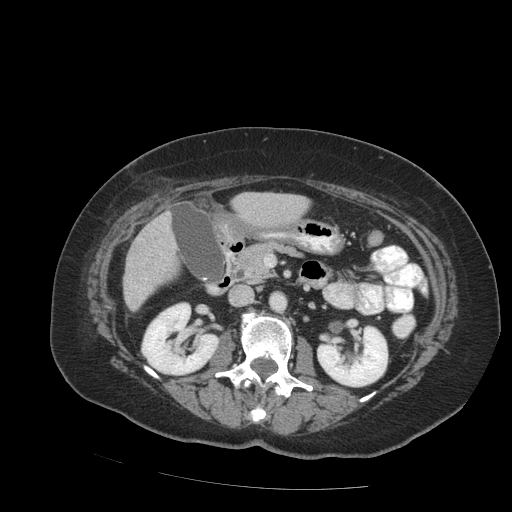
Contrast-enhanced abdominal CT (liver protocol), one axial slice; position 32 of 99 along the scan axis; reconstruction kernel STANDARD; 140 kVp; soft-tissue window (W 400 / L 40 HU); 512 × 512 image matrix, field of view 400 × 400 mm. From the clinical record (not read from this slice): diagnosis: hepatocellular carcinoma (patient treated with transarterial chemoembolisation; whether this scan precedes or follows treatment is not stated here); TNM stage (as recorded): Stage-IVB; Child-Pugh class: A; tumour differentiation: moderately differentiated; tumour nodularity: uninodular.
Outlined on this slice (semi-automatic segmentation, software-assisted and operator-edited):
- liver parenchyma outside the tumour (the mass and vessels are separate outlines, so this box may not span the whole liver): bounding box <124,212,176,310> (left, top, right, bottom; pixels)